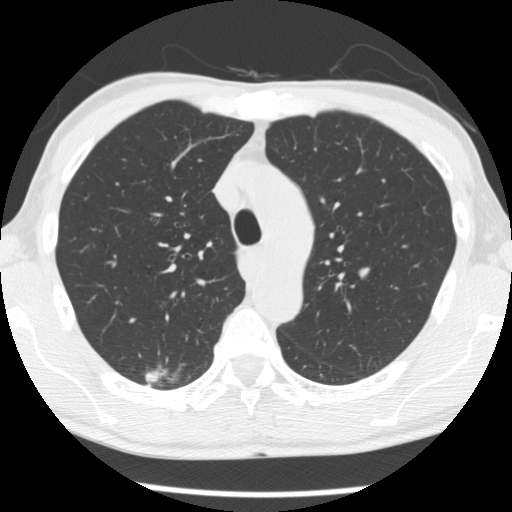
Chest CT (low-dose screening protocol), one axial image, baseline annual screen, lung window (W 1500 / L -600 HU), 2.5 mm slice thickness, 120 kVp, 512 × 512 image matrix. Male participant, aged 66 years at enrolment. Former smoker at enrolment.
Lesion marked by an expert reader, box from (x=134, y=356) to (x=187, y=396) px. The screening reader recorded 4 non-calcified nodules or masses ≥4 mm on this exam; which of them this box marks is not recorded. Later outcome: lung cancer diagnosed 503 days after this screen (after the second annual screen) — adenocarcinoma, NOS, right upper lobe, undifferentiated (G4), stage IA (AJCC 6th edition), 20 mm at pathology.